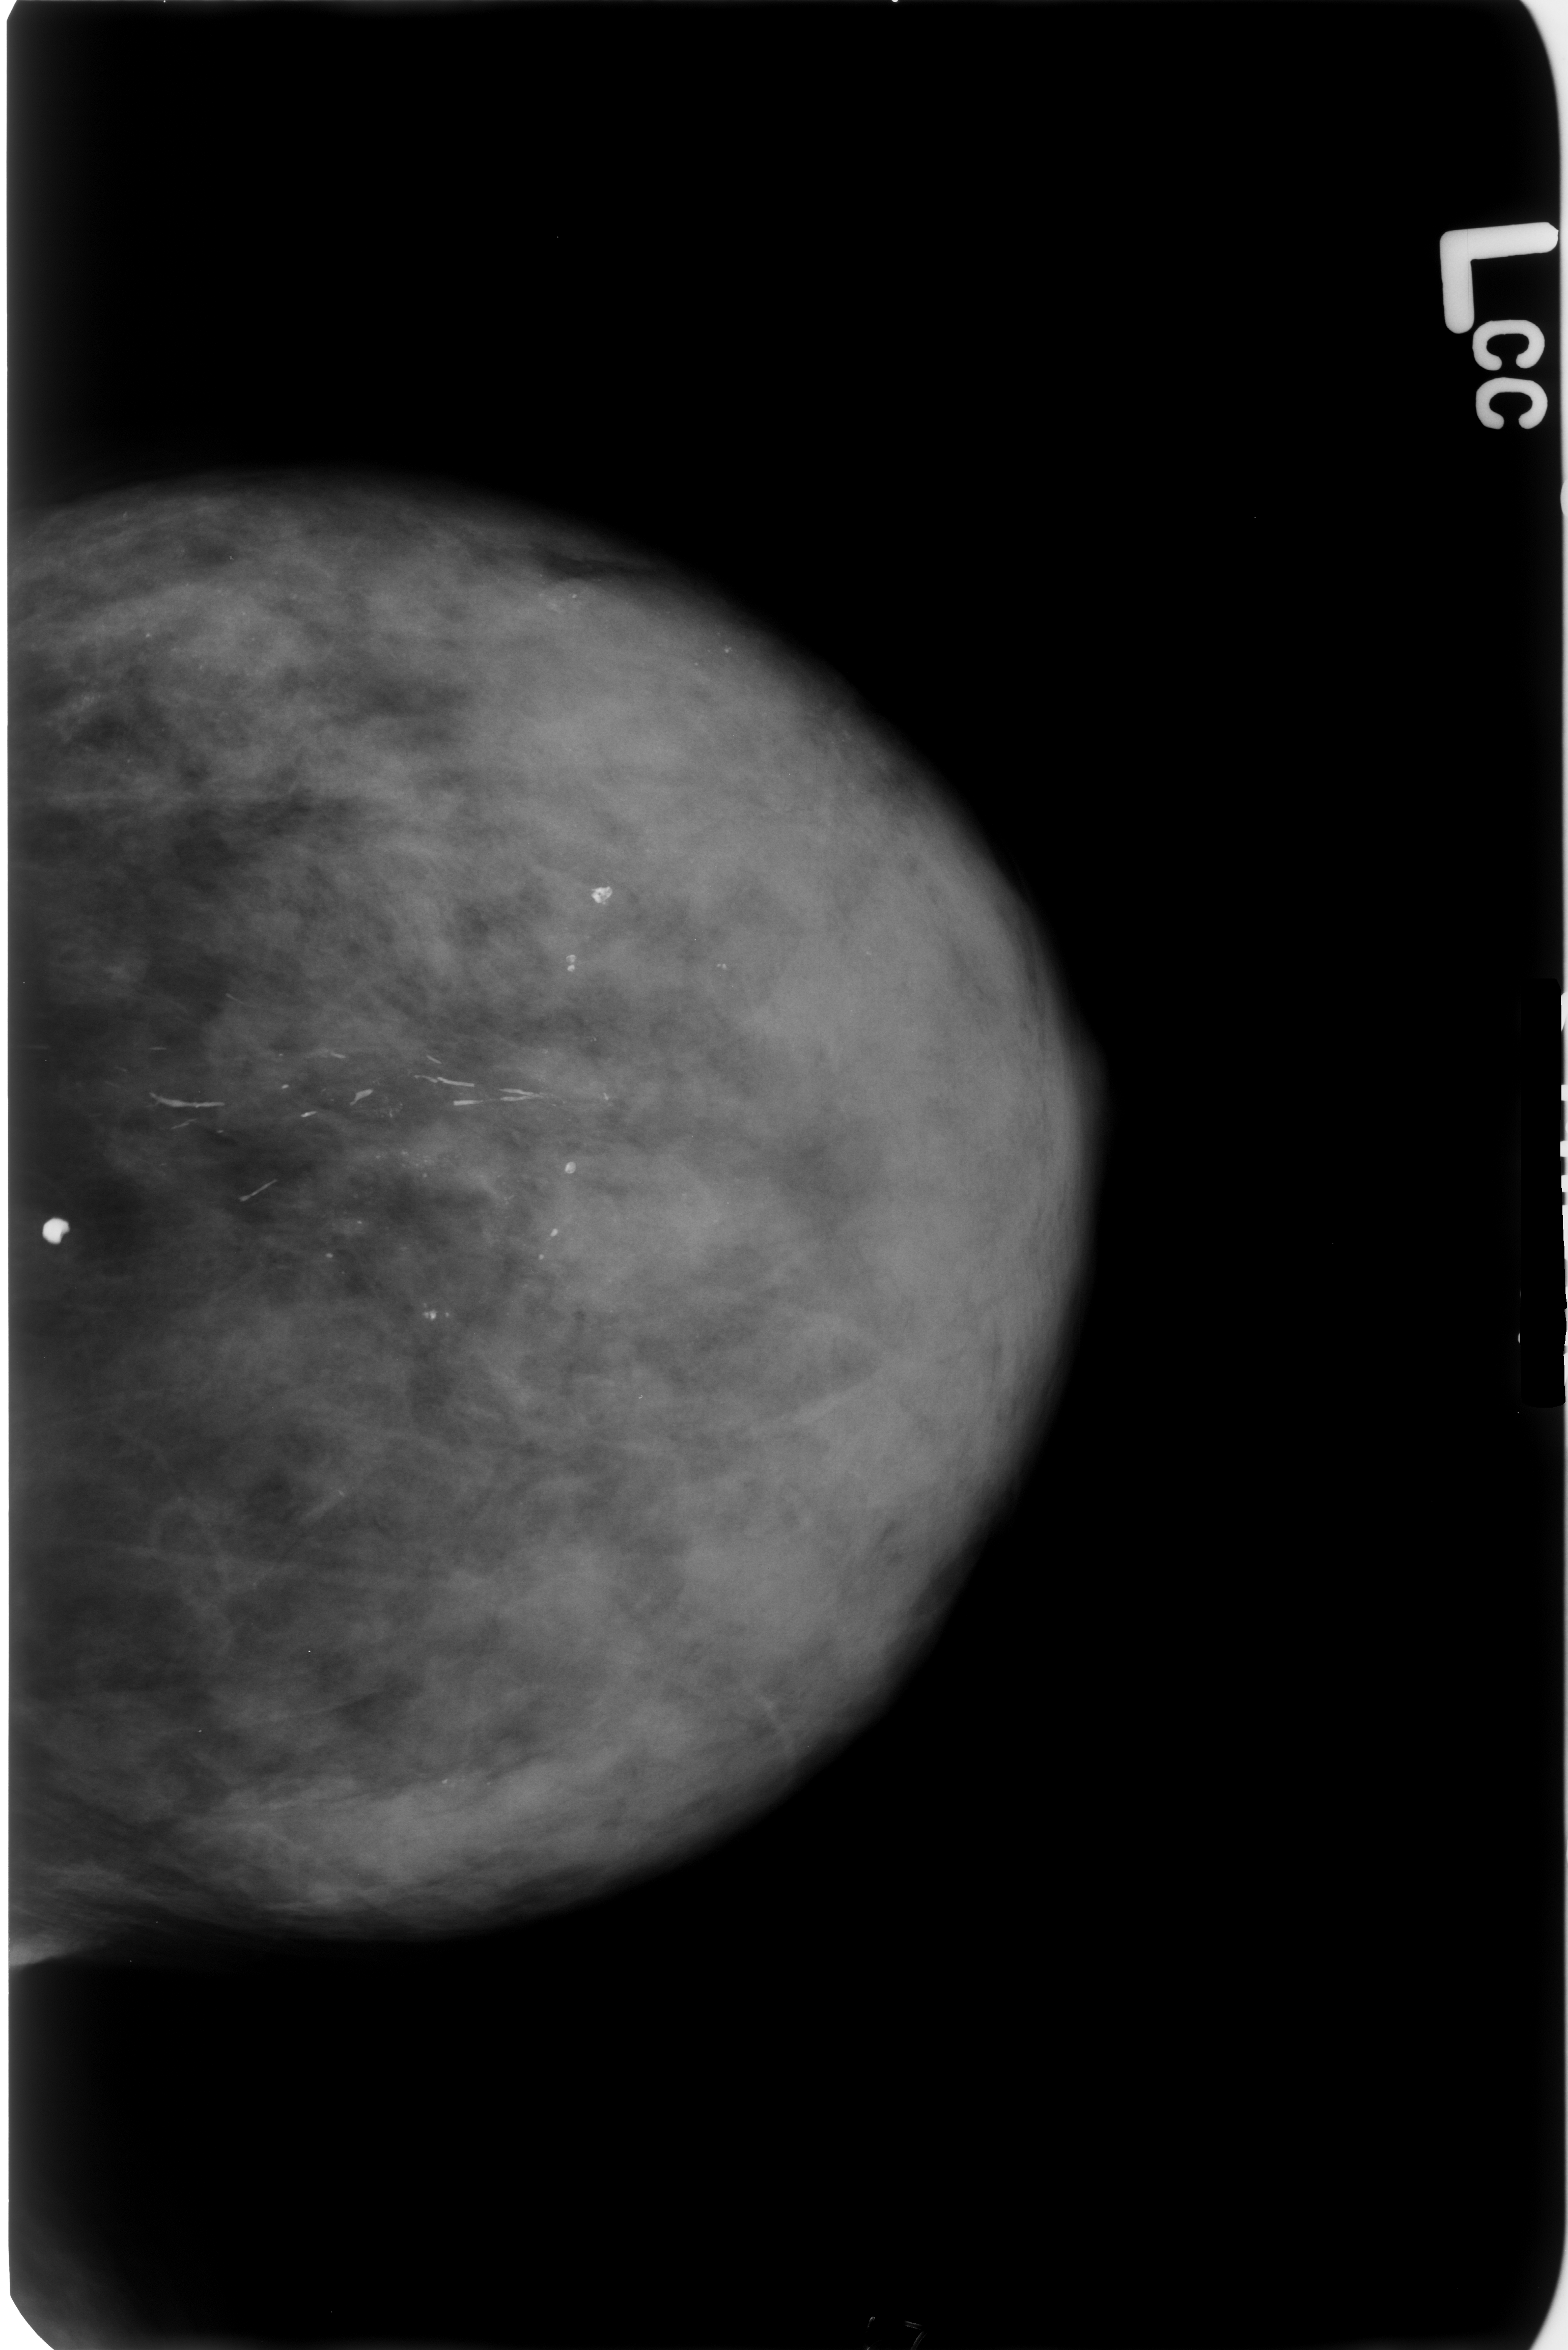
Scanned film-screen mammogram; left breast; craniocaudal (CC) view; BI-RADS breast density category 4 (scale 1–4).
- Marked abnormality: calcifications, morphology punctate / lucent center, distribution regional; BI-RADS assessment category 2; benign without callback (not worked up further).